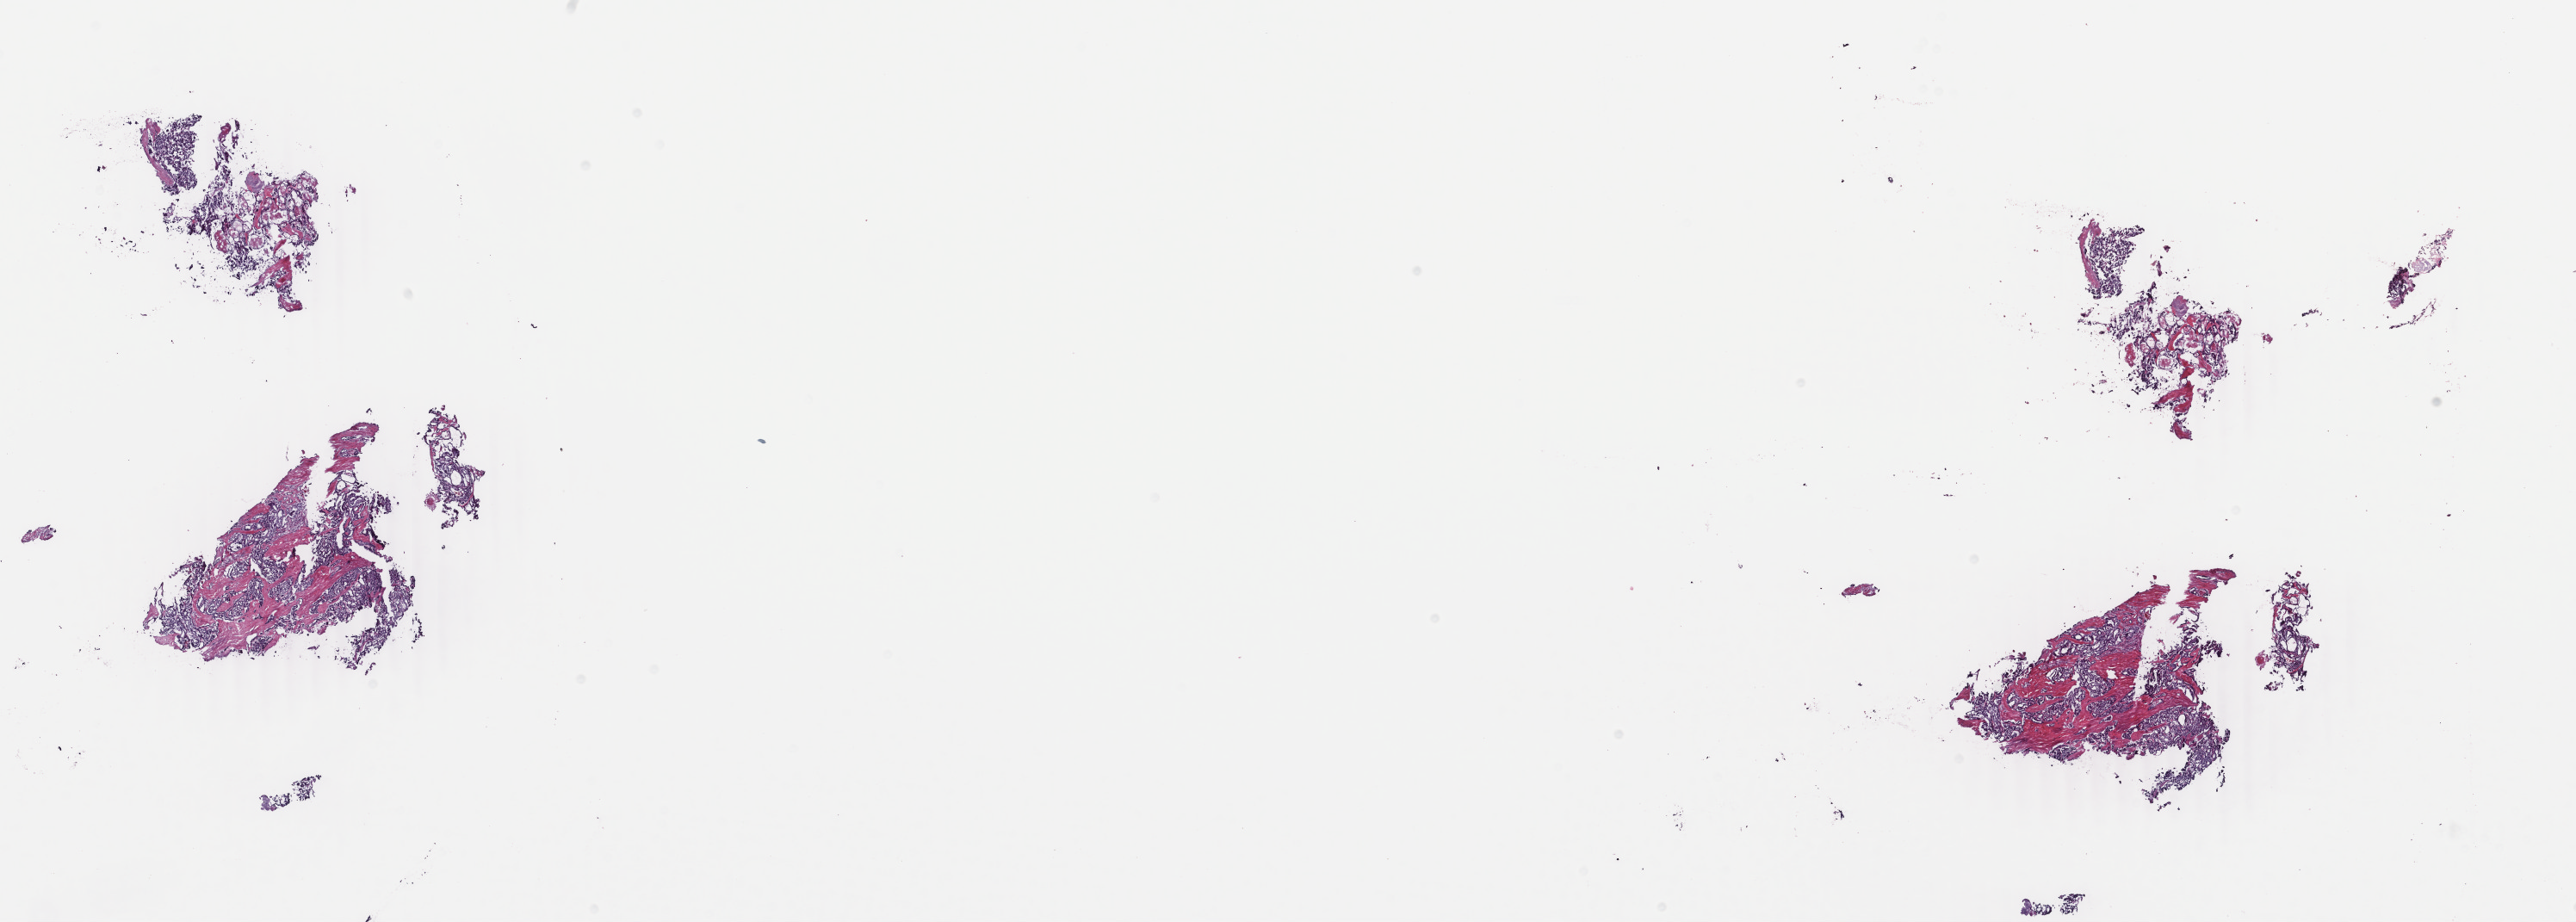
Digitized H&E-stained tissue section (whole slide) — whole scanned area (about 23.8 x 8.5 mm) shown as a low-resolution overview. Frozen section from the bottom of the tissue portion. Sample: primary tumour, thyroid. Male patient; age at initial diagnosis 60 years. Slide review estimates, as recorded: tumour cells 95%, tumour nuclei 95%, normal cells 0%, stromal cells 5%, necrosis 0%. Infiltration values recorded for this section: lymphocyte infiltration 0%, monocyte infiltration 0%, neutrophil infiltration 0%.
AJCC pathologic stage: III (7th edition). Diagnosis: Papillary adenocarcinoma, NOS (thyroid gland).